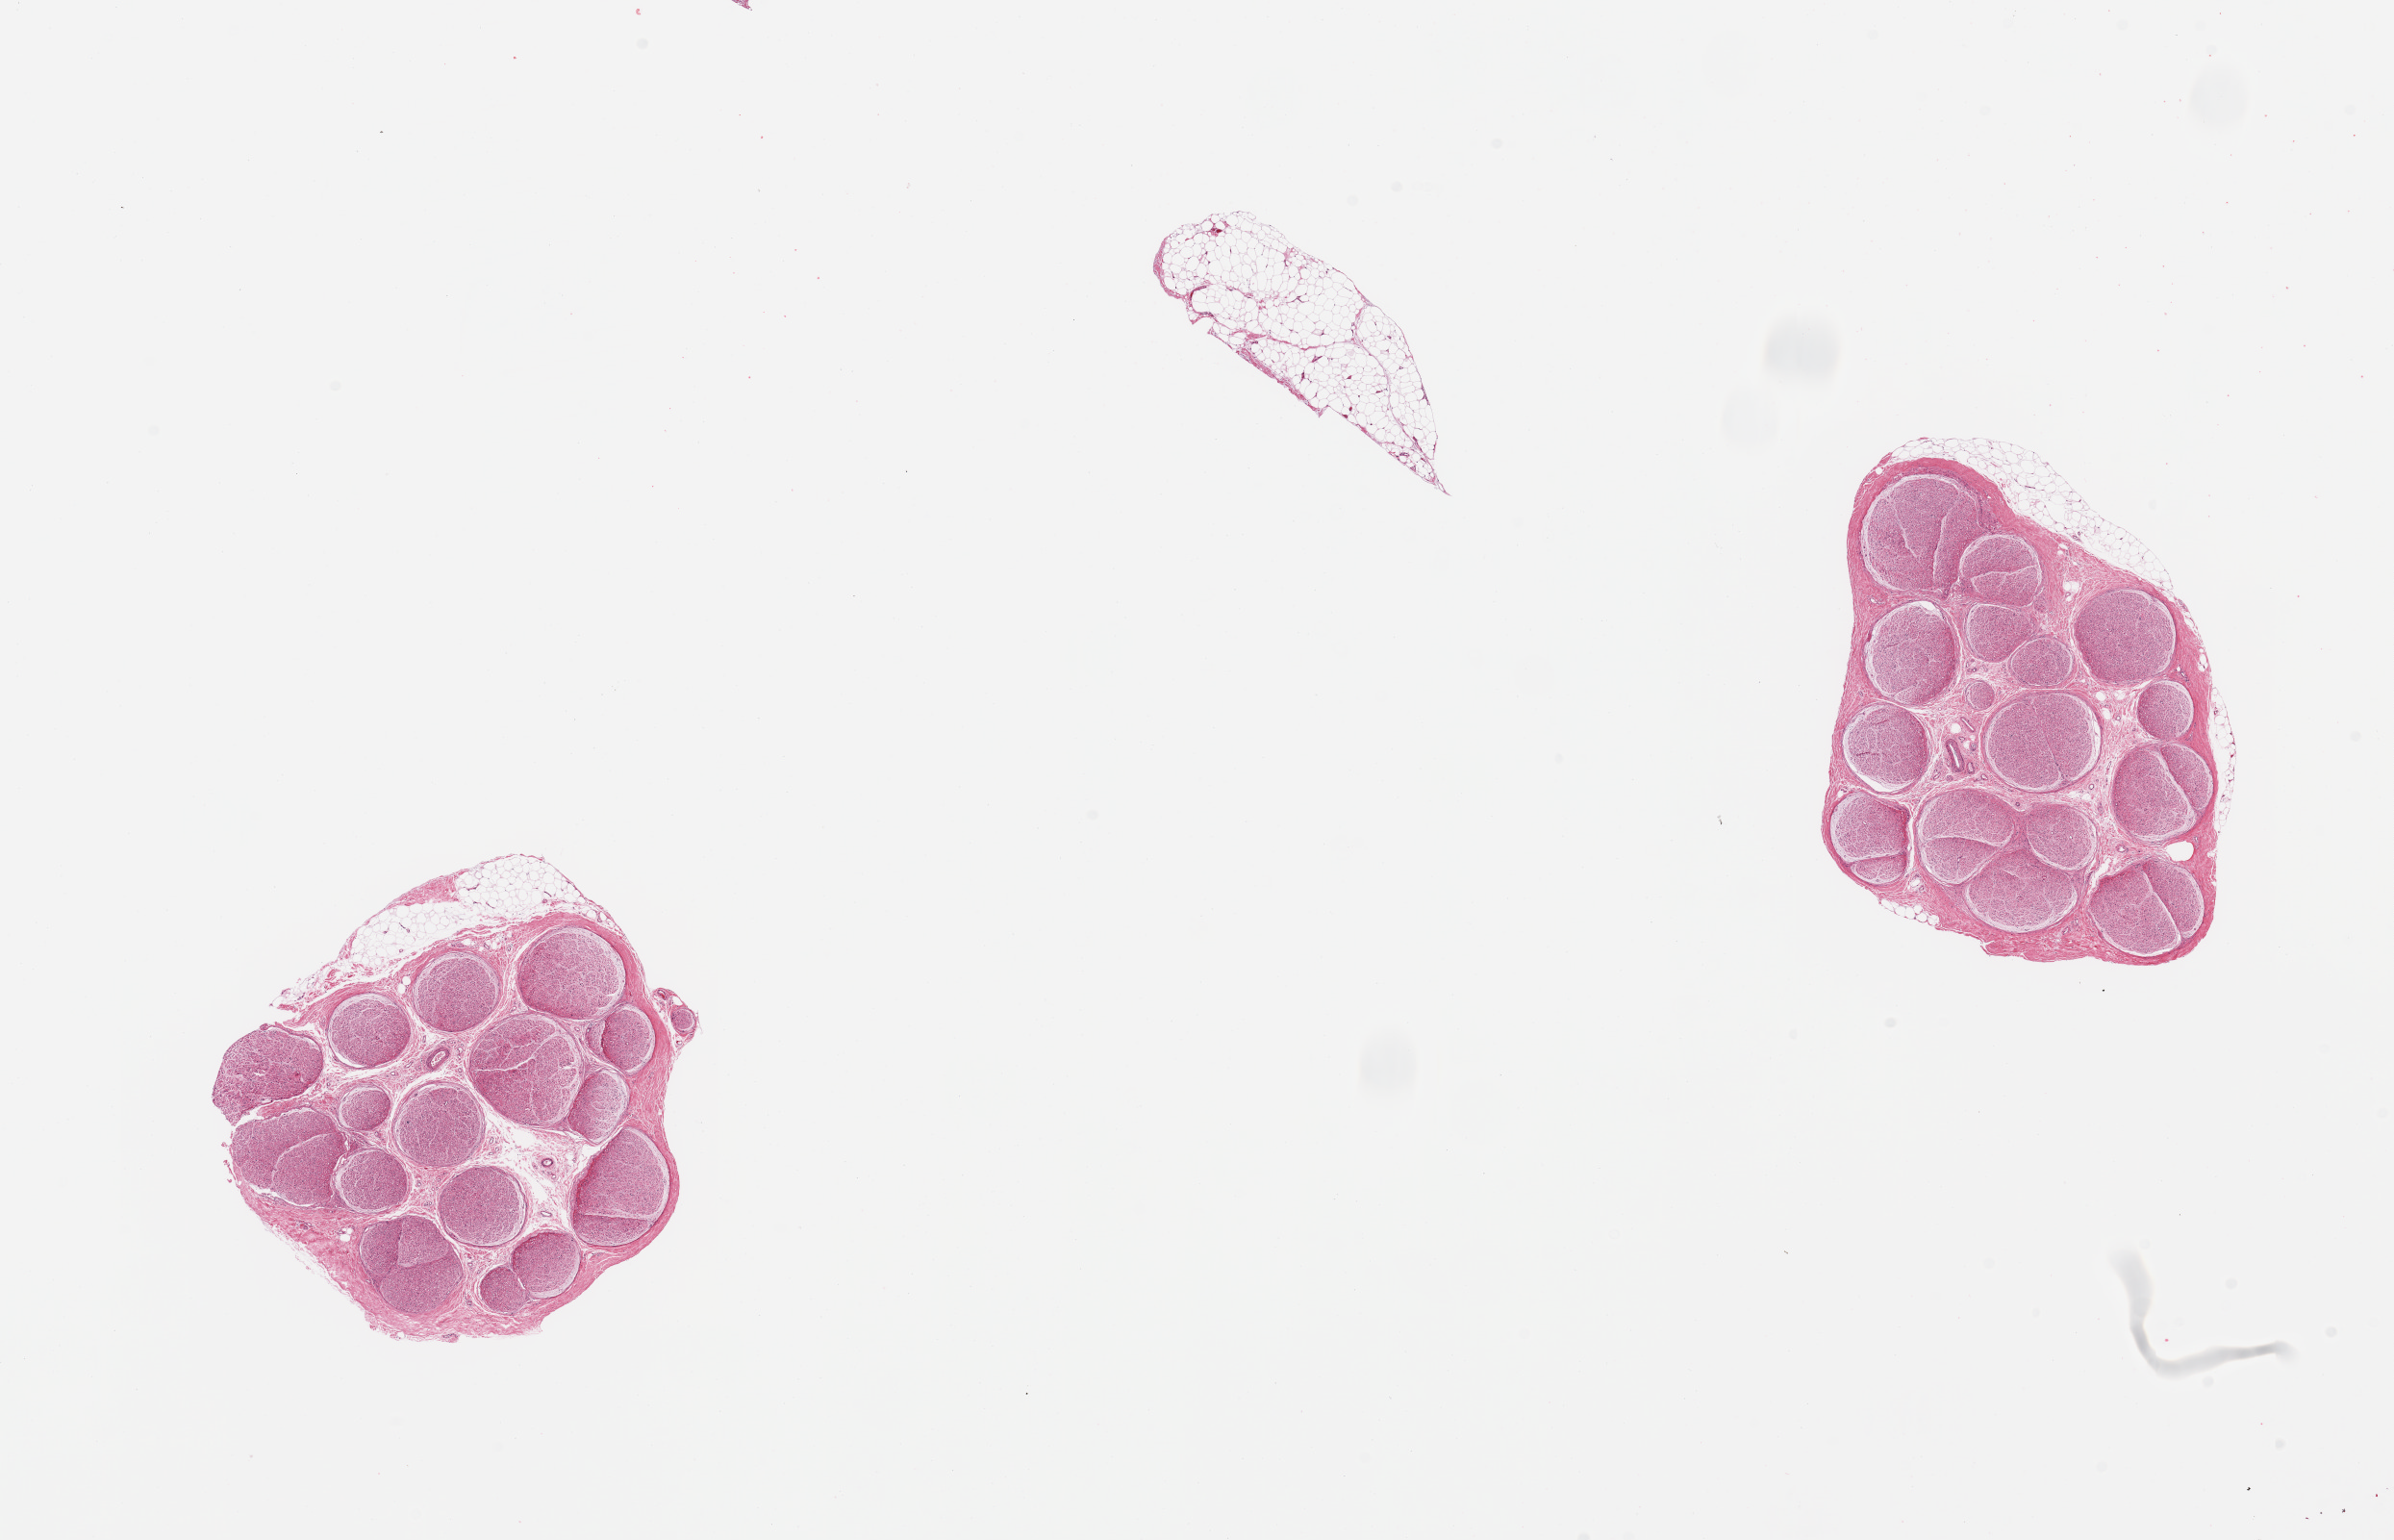
H&E whole-slide image, whole scanned area (about 19.7 x 12.7 mm) shown as a low-resolution overview, PAXgene-fixed paraffin-embedded (PFPE) section, sampled site (target tissue): tibial nerve, donor tissue sample. Donor sex: female.
Pathologist's review note for this sample: 2 pieces; essentially well trimmed, <10% attachment of fat.